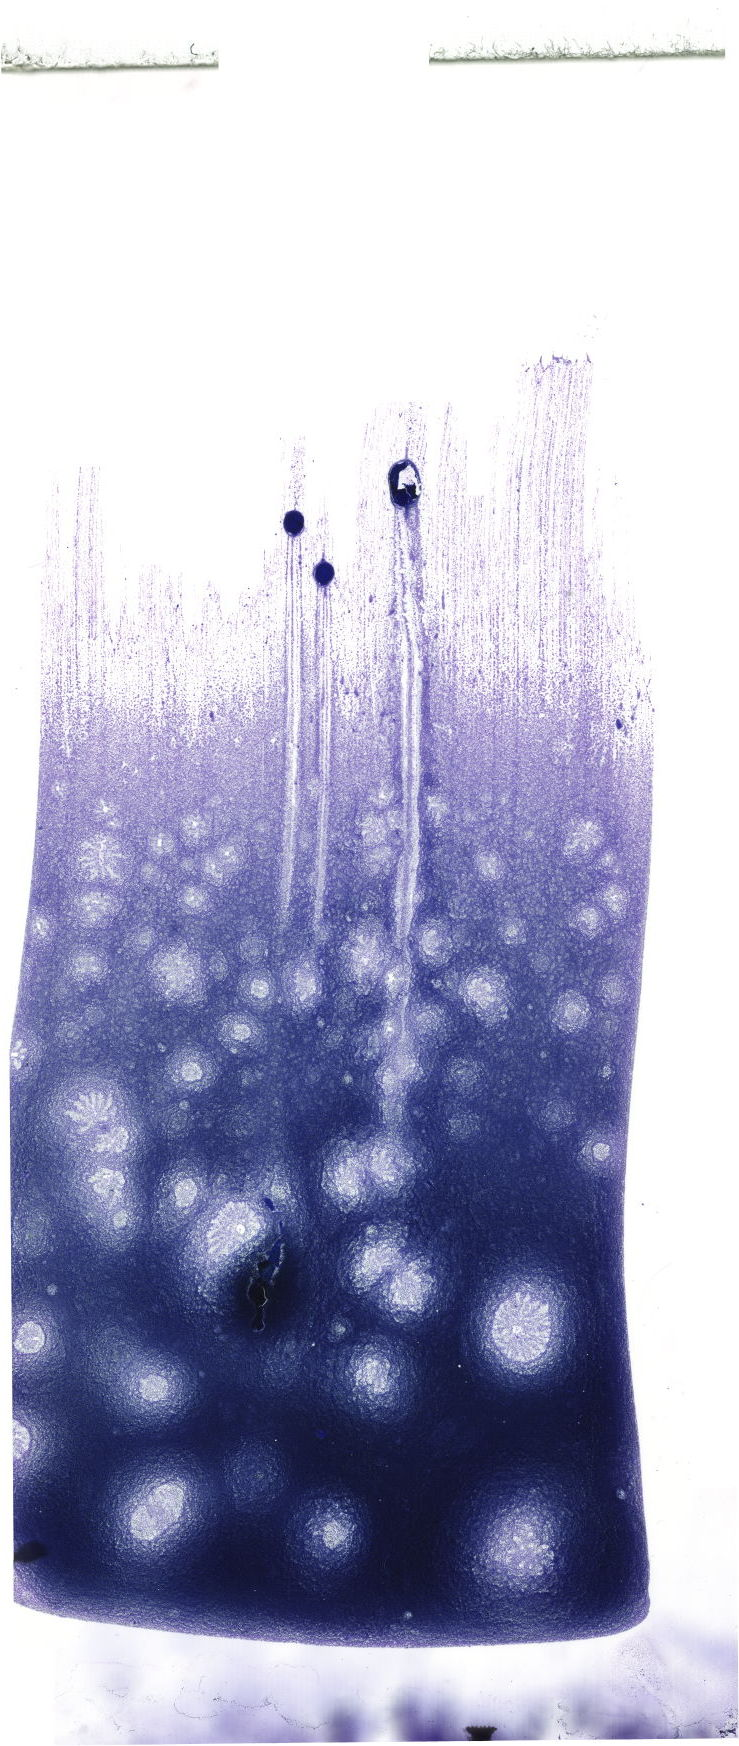
Whole-slide image of a May-Grünwald–Giemsa-stained bone marrow aspirate smear, shown as a low-resolution overview of the whole scanned area (about 20.9 x 49.5 mm). Female patient.
Diagnosis: Chronic Phase Chronic Myeloid Leukemia, BCR-ABL1 Positive.